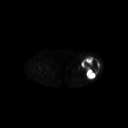
FDG PET of an extremity soft-tissue mass (from a PET/CT study), one axial slice; slice 222 of 267 in the series (ordered by position); 3.27 mm slice thickness; 128 × 128 image matrix. Patient: female, 62 years. Case-level facts recorded for this patient, not image findings: histological type: undifferentiated – high grade; grade: high; site of the primary tumour: left thigh.
Annotated regions visible in this slice (expert contour drawn on MRI and transferred to this co-registered scan by the dataset authors):
- gross tumour volume including surrounding oedema: bounding box [x1, y1, x2, y2] px = [81, 56, 100, 79]
- gross tumour volume (mass): [81, 56, 100, 79]